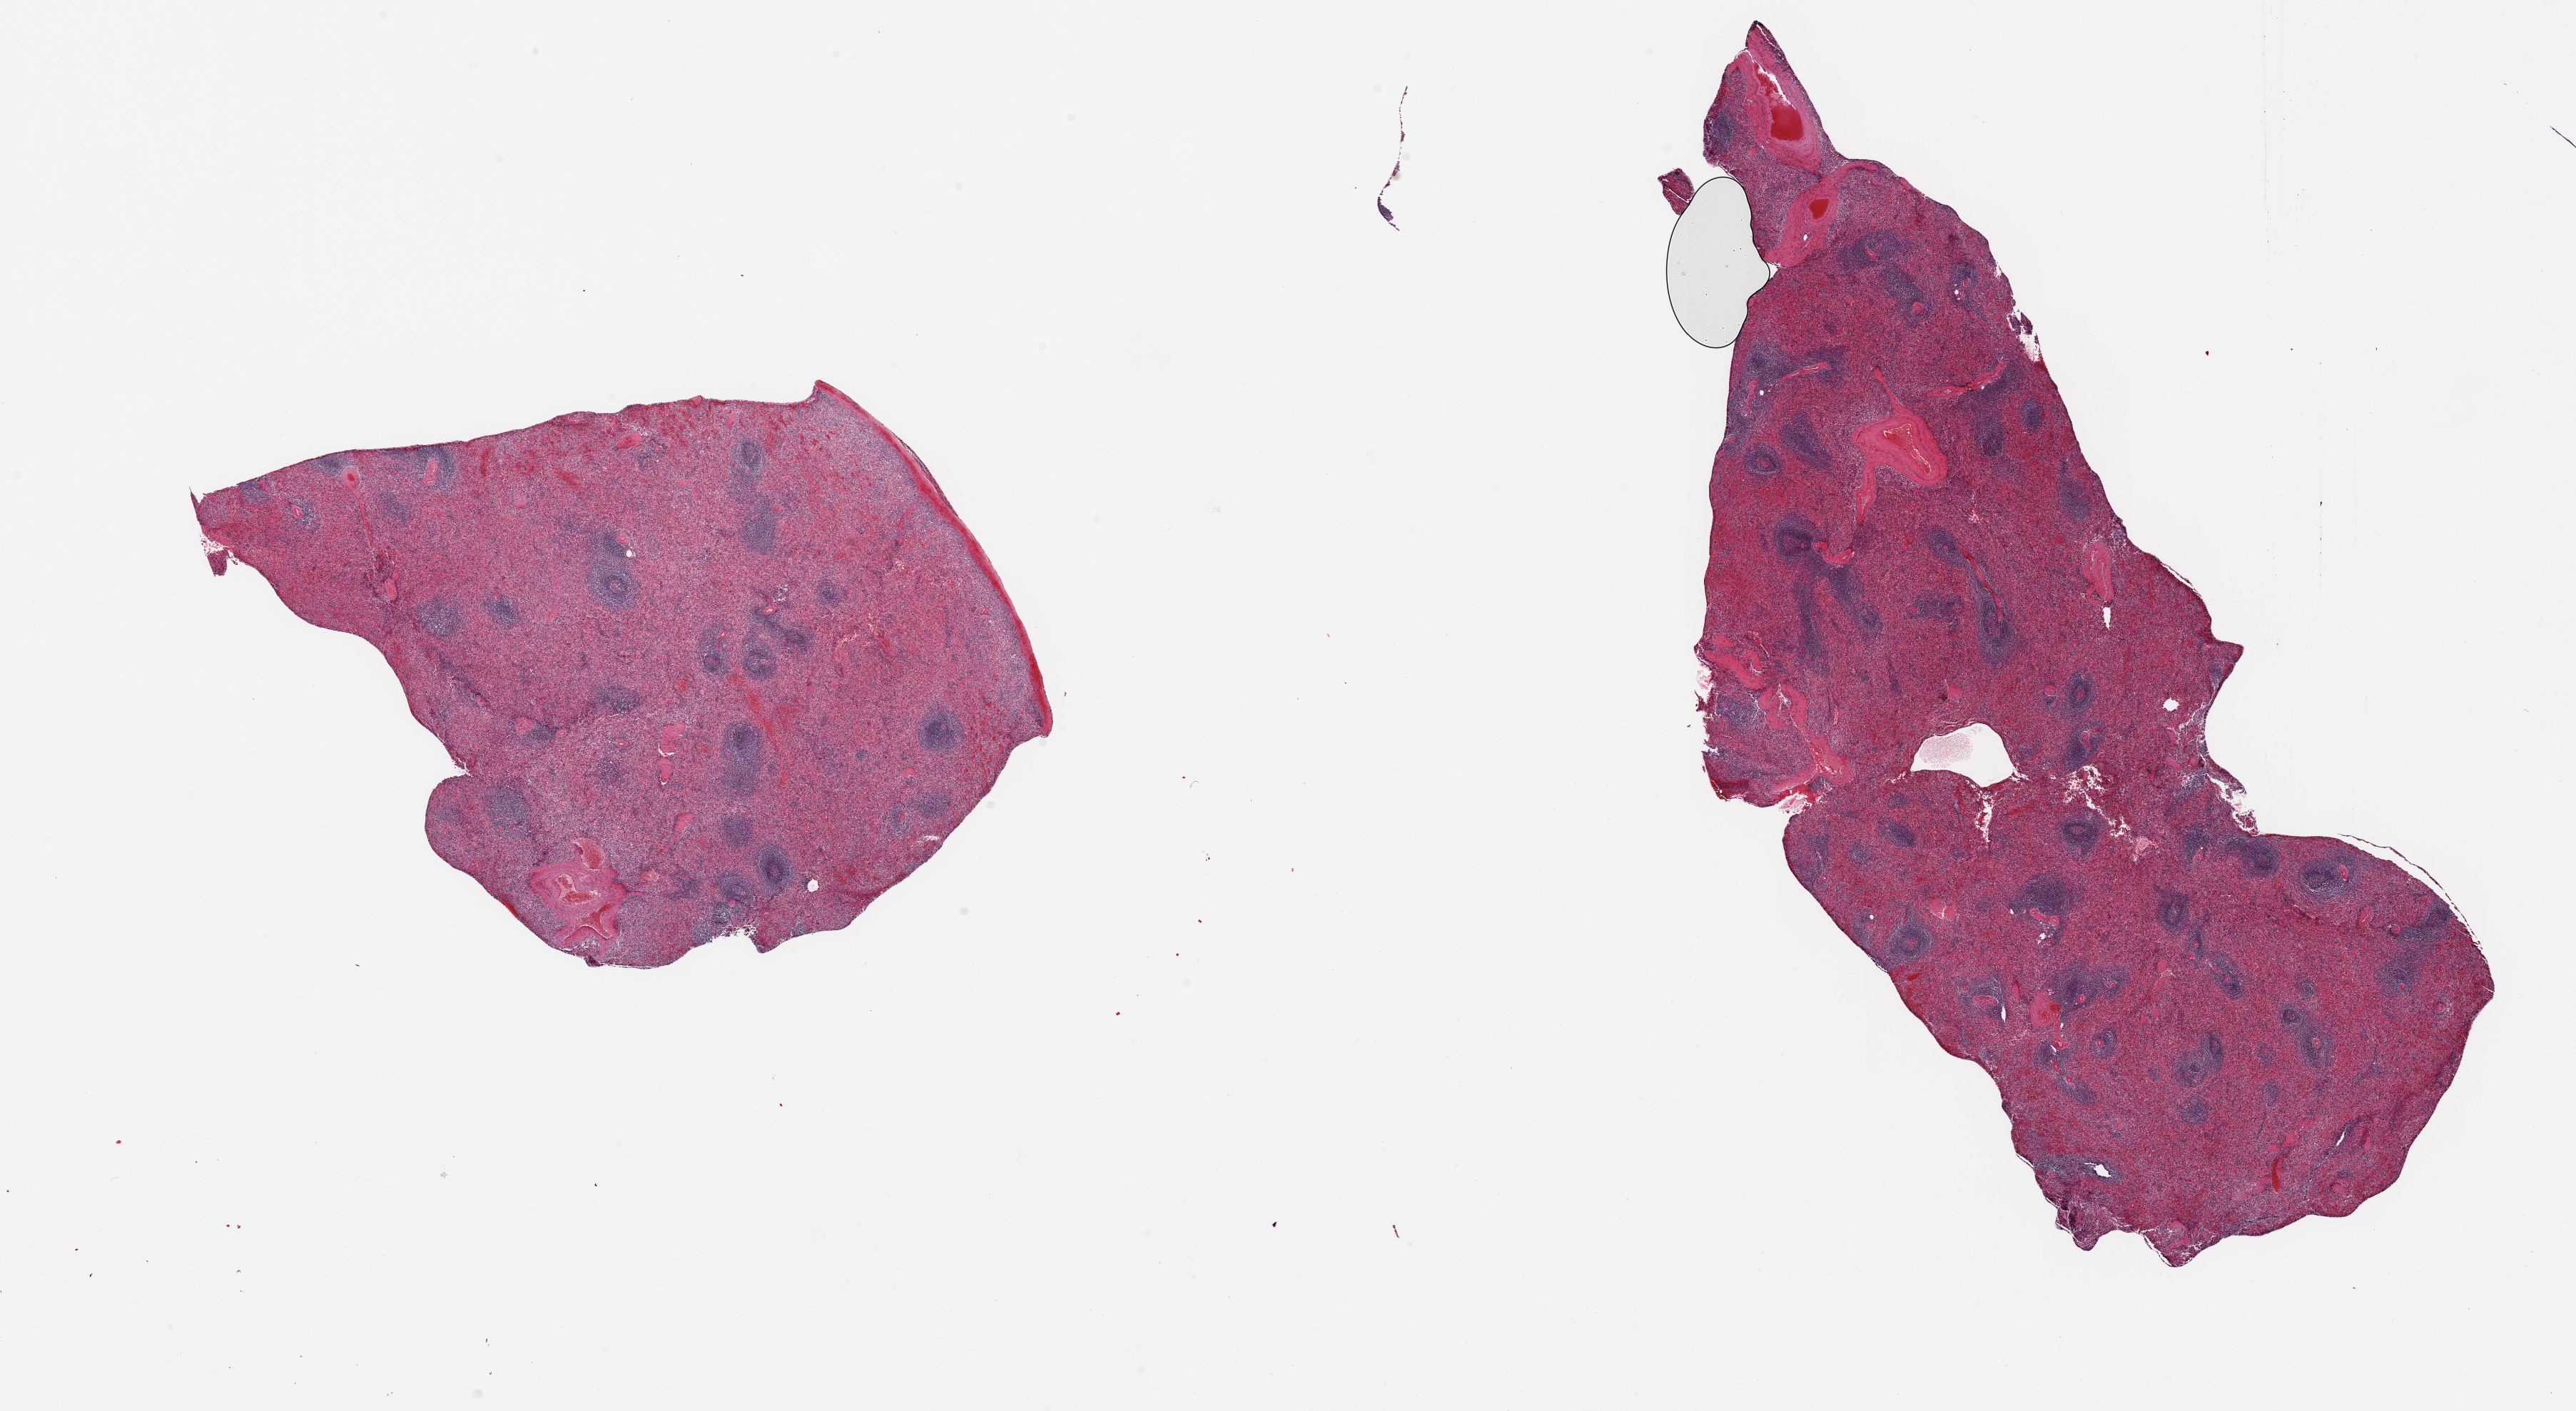
Haematoxylin and eosin whole-slide image, shown as a low-resolution overview of the whole scanned area (about 28.5 x 15.6 mm). PAXgene-fixed paraffin-embedded (PFPE) section. Sampled site (target tissue): spleen. Tissue donor sample. Female donor.
Review note (as recorded): 2 pieces; includes capsule (target is 5mm below capsule), numerous hemosiderin-laden macrophages.